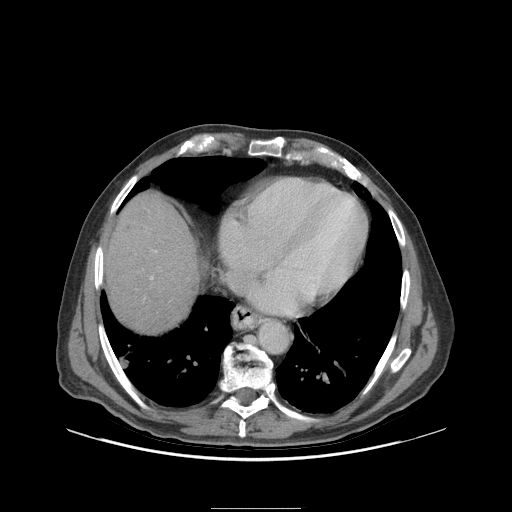
Contrast-enhanced abdominal CT (liver protocol), one axial slice; position 90 of 105 along the scan axis; 140 kVp; soft-tissue window (W 400 / L 40 HU); 2.5 mm slice thickness; 512 × 512 image matrix, field of view 440 × 440 mm. From the clinical record (not read from this slice): diagnosis: hepatocellular carcinoma (patient treated with transarterial chemoembolisation; whether this scan precedes or follows treatment is not stated here); TNM stage (as recorded): Stage-I; Child-Pugh class: A; tumour nodularity: uninodular; tumour size: 5.1 cm.
Outlined on this slice (semi-automatic segmentation, software-assisted and operator-edited):
- liver parenchyma outside the tumour (the mass and vessels are separate outlines, so this box may not span the whole liver): bounding box (x1, y1, x2, y2) in pixels: (104, 192, 198, 330)
- liver vessels: (150, 250, 156, 280)